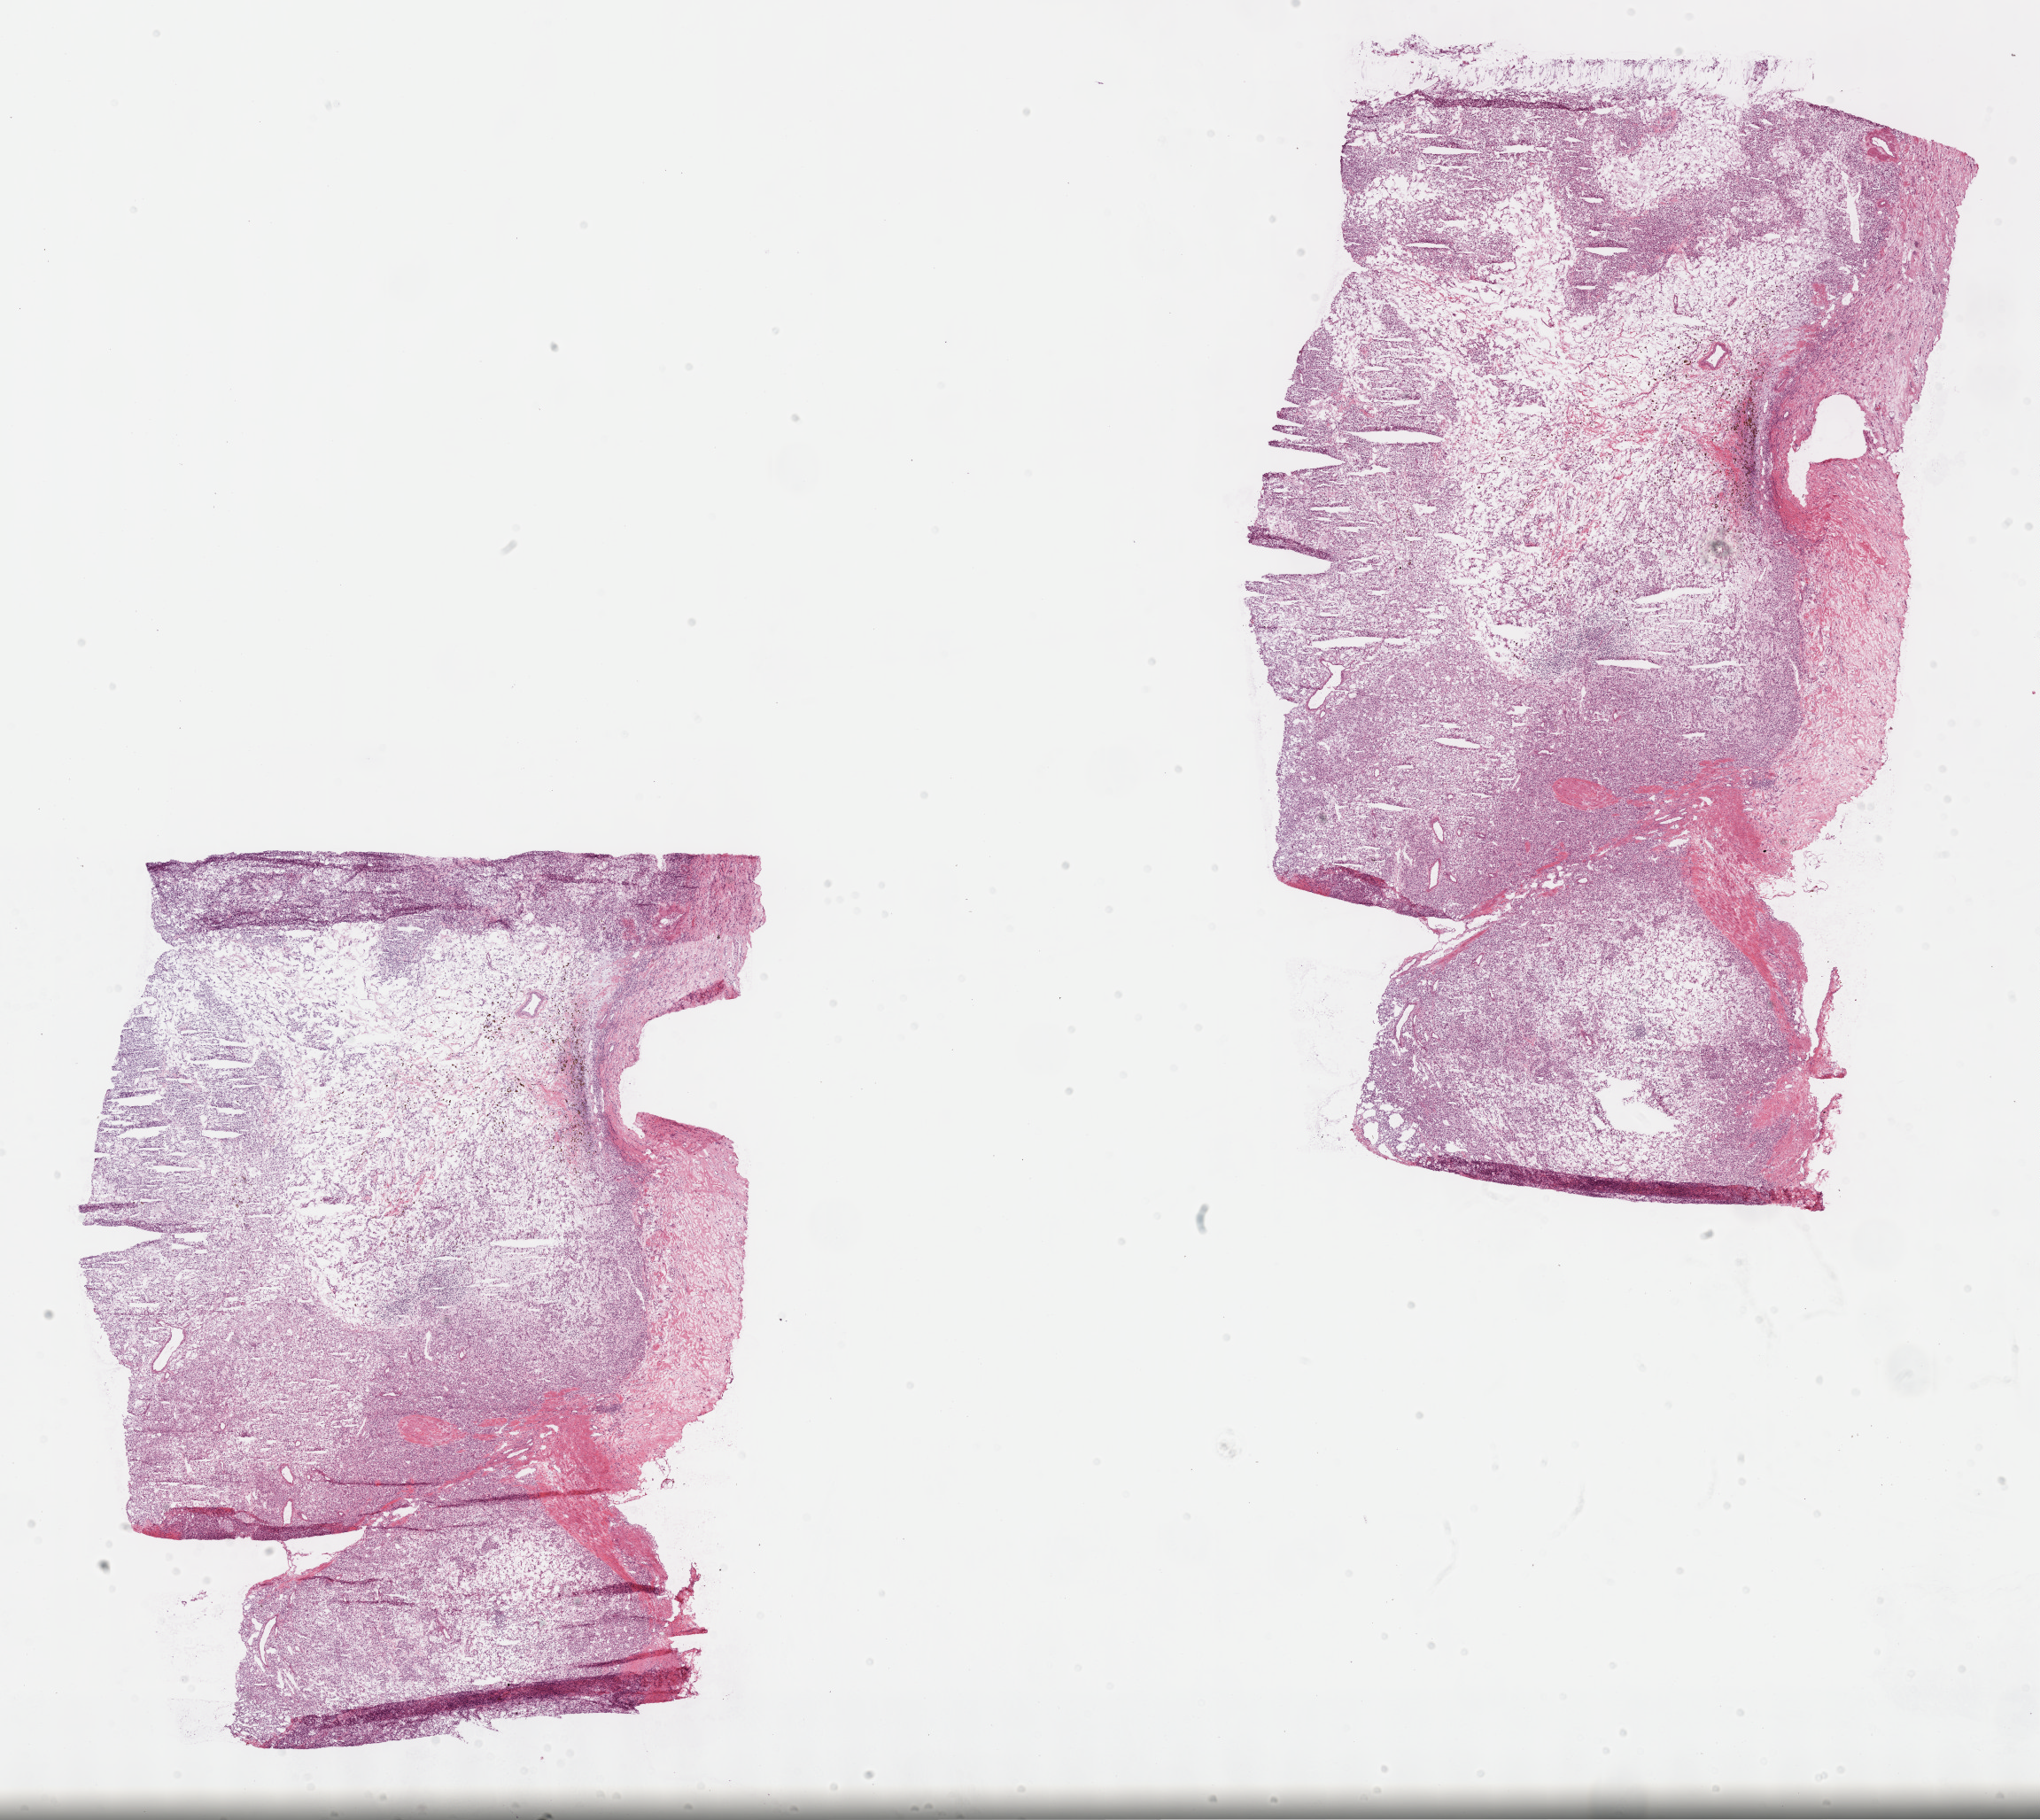
Whole-slide histology image, H&E — low-resolution overview of the scanned area, about 18.6 x 16.6 mm (acquisition: 40x scan). Frozen section. Primary tumour sample from the kidney. Male, age 79 years at initial diagnosis. Histologic grade: G2 (moderately differentiated). Pathologist review of this section (percent, as recorded): tumour cells 90%, tumour nuclei 80%, normal cells 0%, stromal cells 10%, necrosis 0%.
Laterality: right. Histologic diagnosis: Clear cell adenocarcinoma, NOS. AJCC pathologic stage: I.